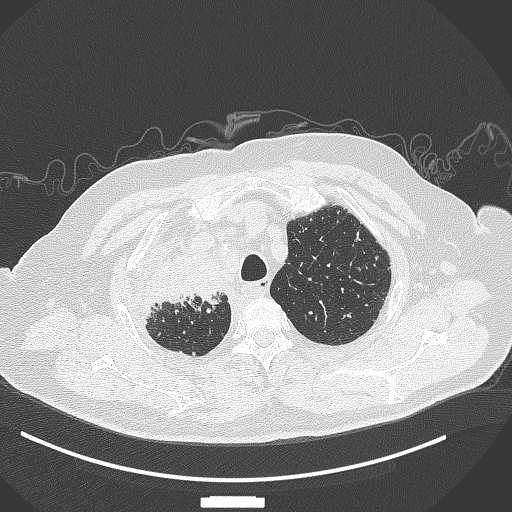
Chest CT, one axial slice. Slice 307 of 384 in the series (ordered by position). Lung window (W 1500 / L -600 HU). 1 mm slice thickness. 512 × 512 image matrix. Male patient, age 69 years. From the clinical record (not read from this slice): clinical TNM (as recorded): T4 N3 M1.
Annotated regions visible in this slice (rectangle marked by the reading radiologist):
- lung tumour (recorded histology: adenocarcinoma): bounding box (x1, y1, x2, y2) in pixels: (137, 255, 224, 316)